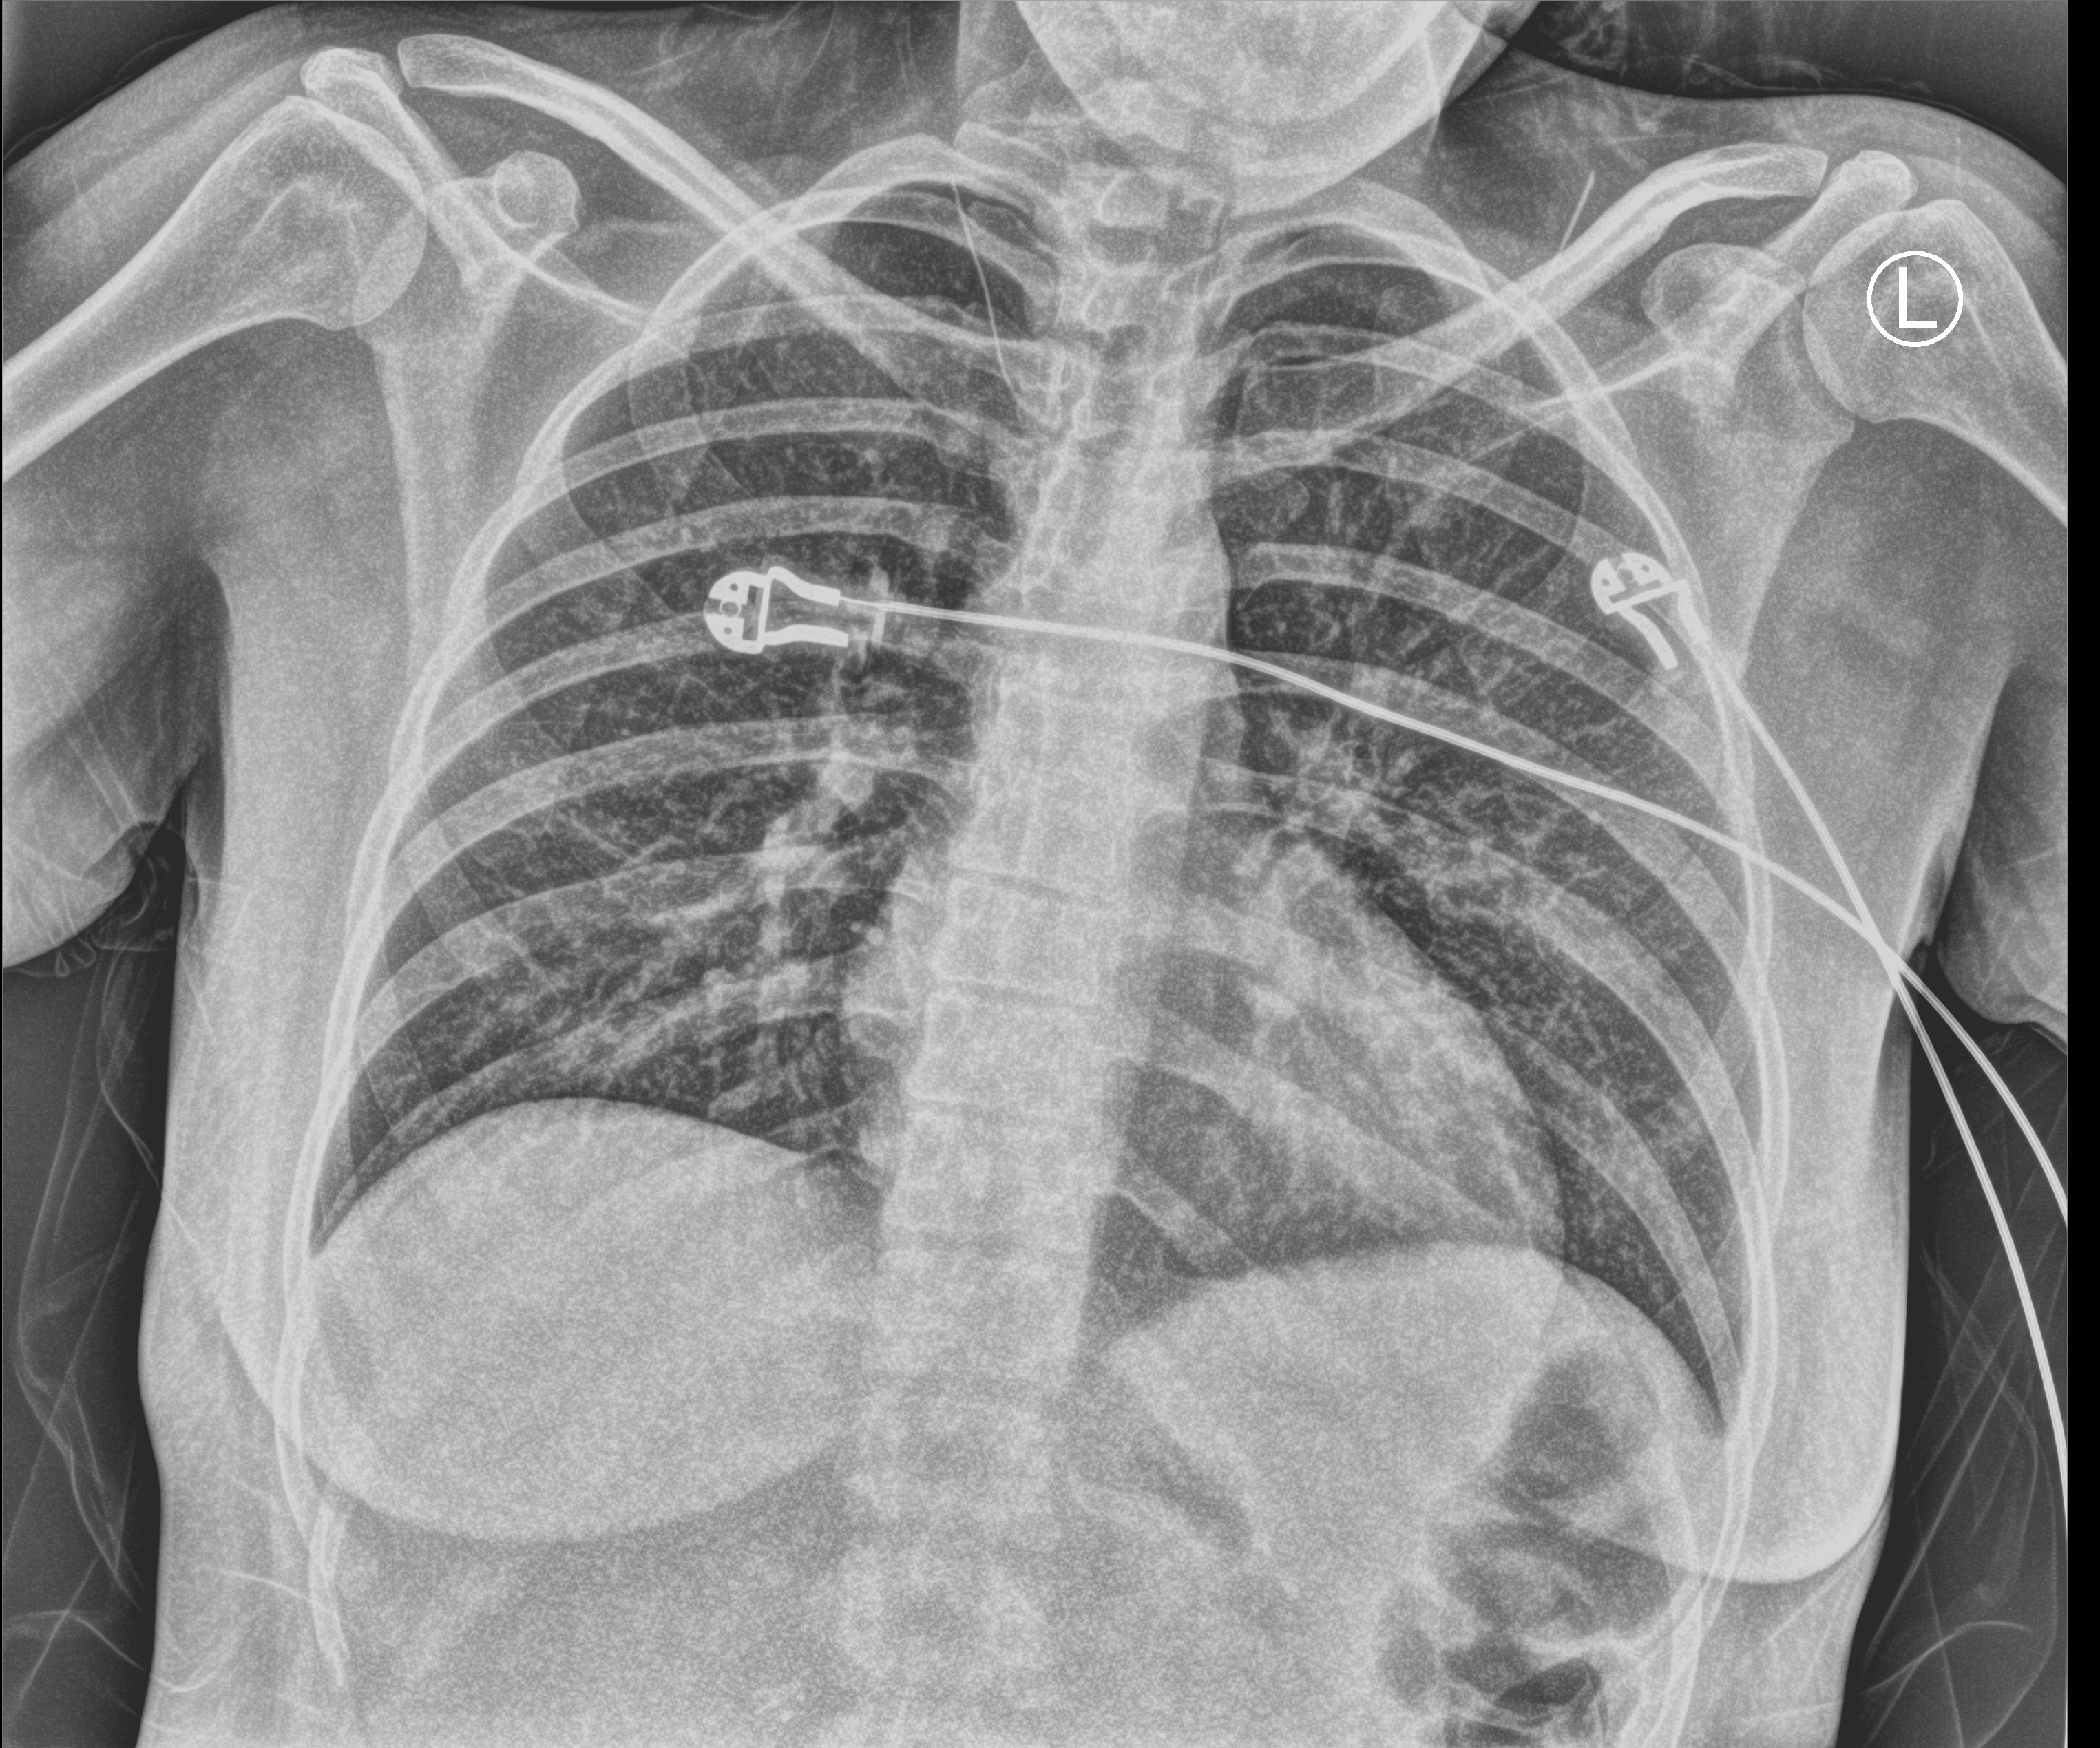
Portable chest radiograph, anteroposterior (AP) projection. Patient hospitalised with COVID-19; female, aged 18–59 years.
Hospital-stay facts (about this admission, not read from this image; timing relative to this image not recorded): mechanically ventilated during this hospital stay: no; admitted to intensive care during this hospital stay: no.